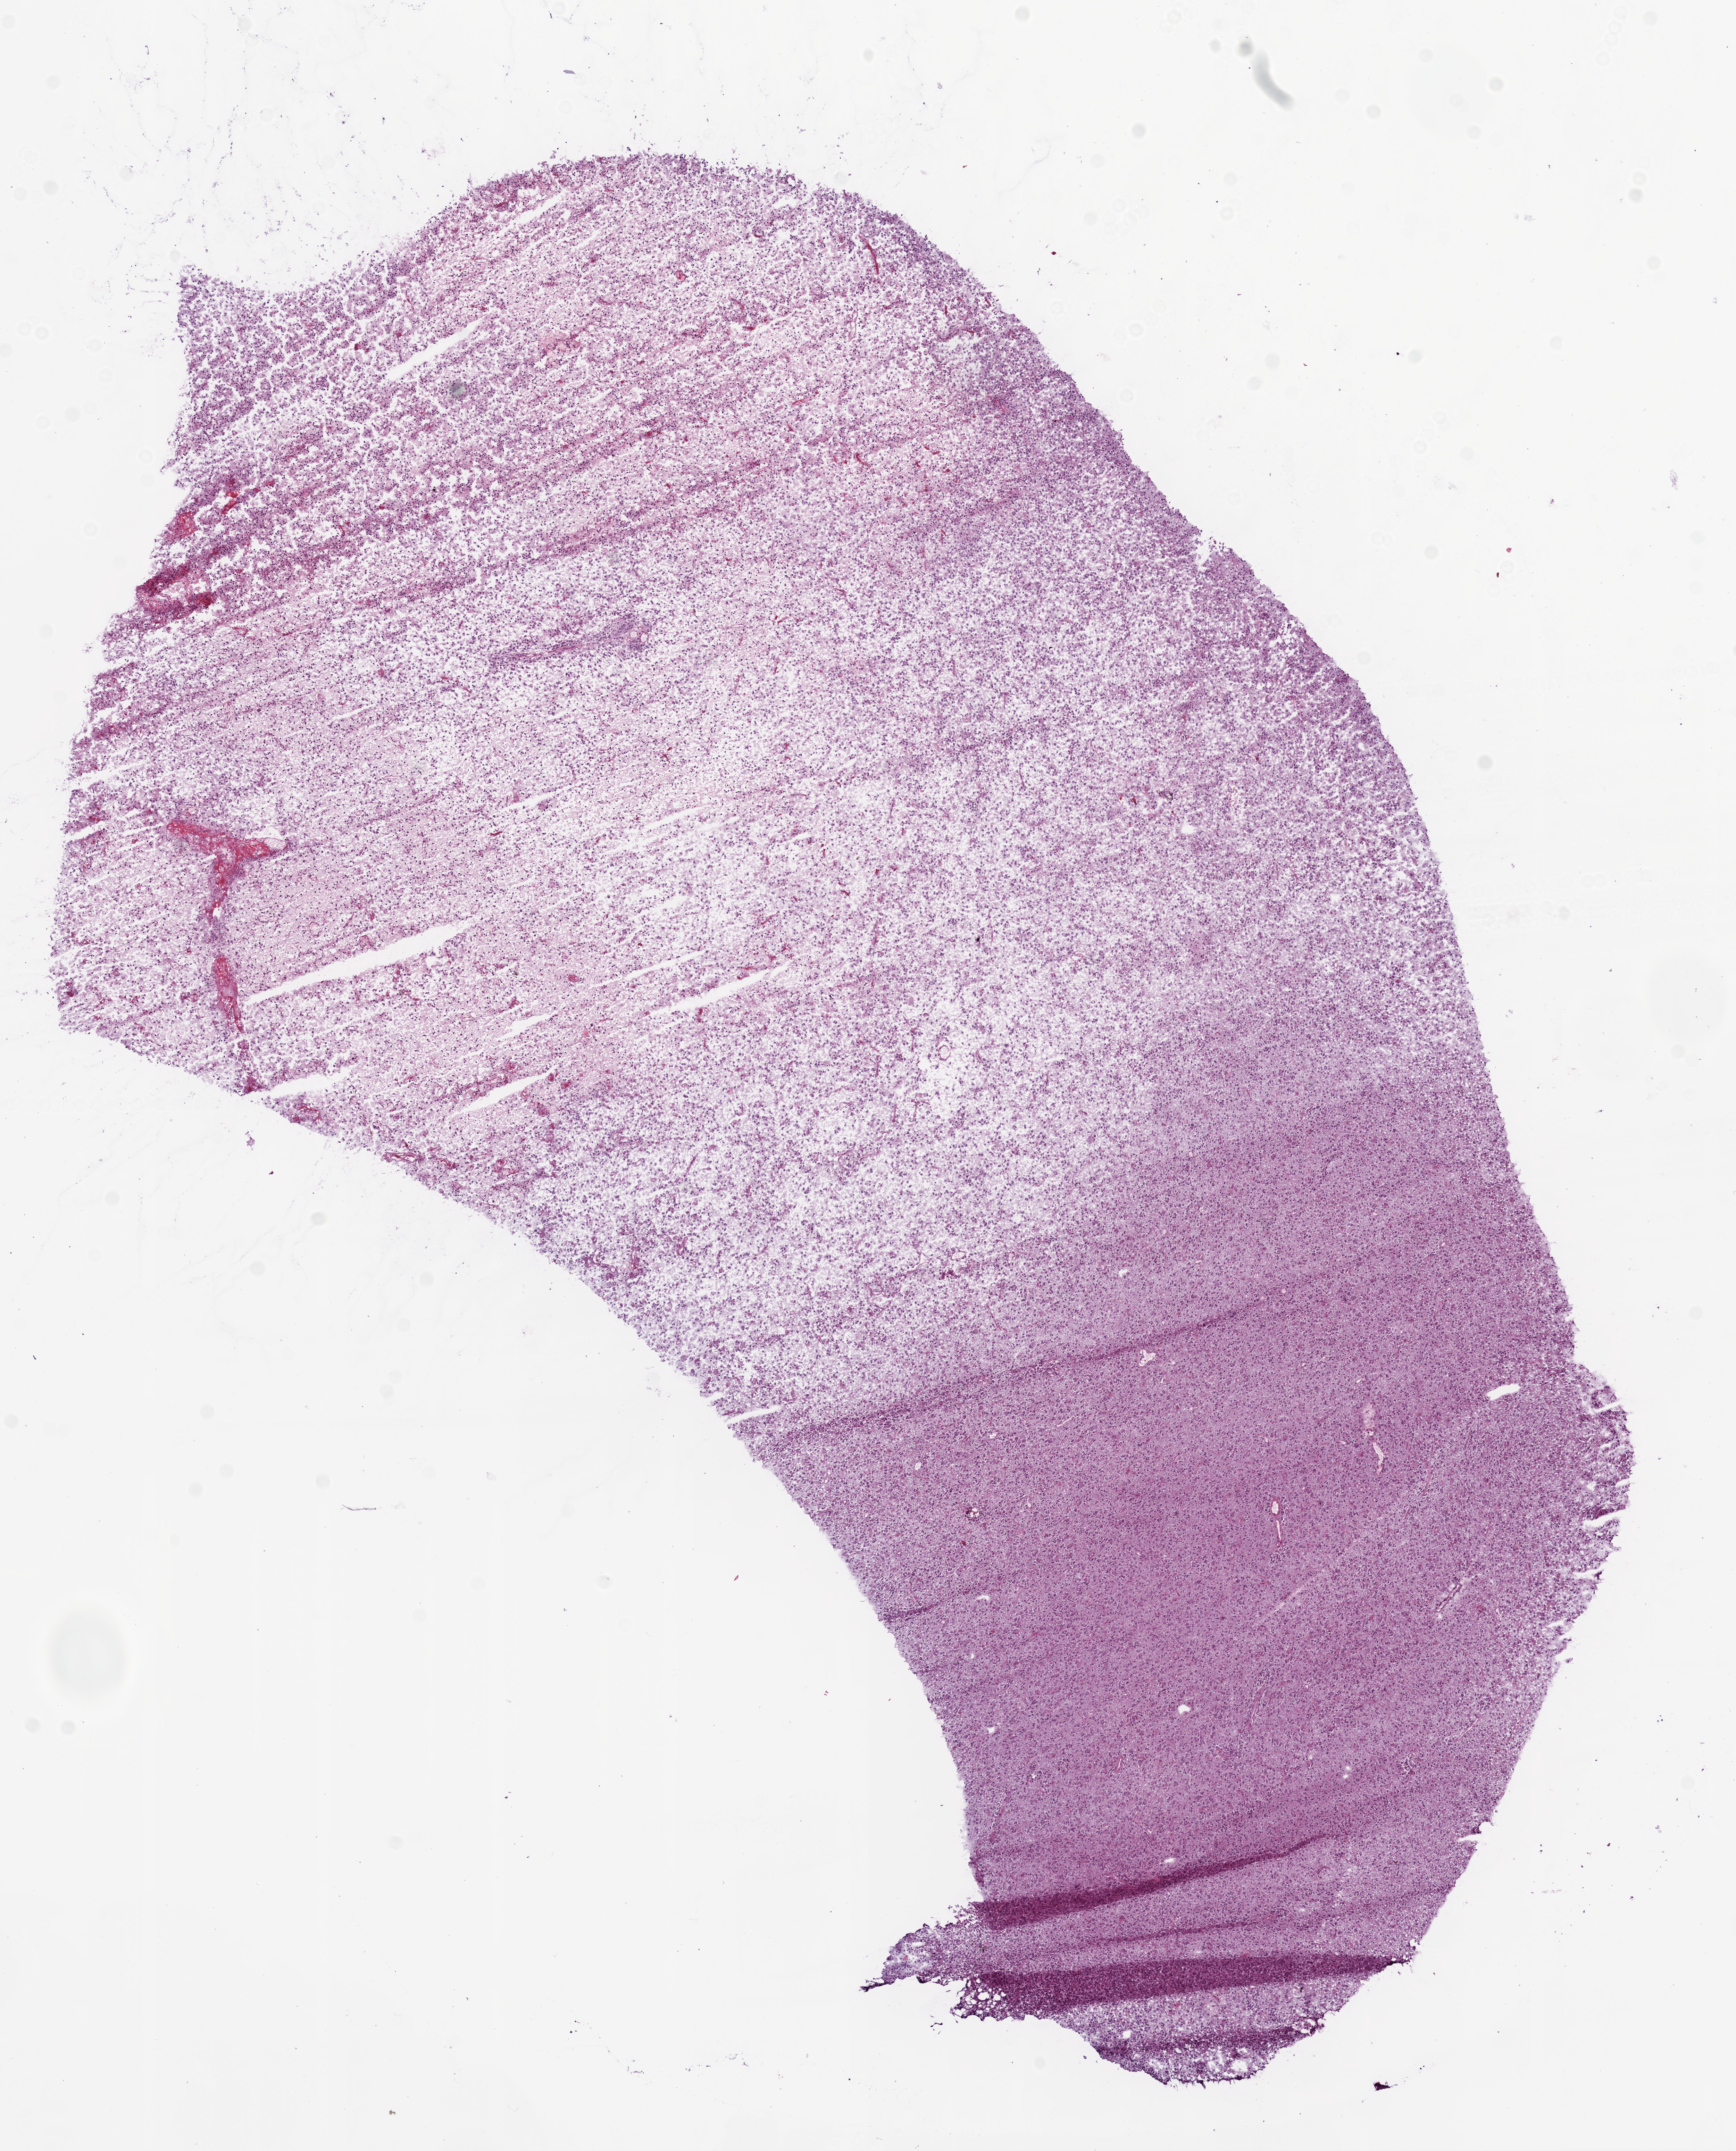
Digitized Hematoxylin and eosin (H&E) stained tissue section (whole slide), shown as a low-resolution overview of the whole scanned area (about 10.0 x 12.4 mm). Frozen section from the bottom of the tissue portion. Brain, primary tumour sample. Patient: male, age at initial diagnosis 45 years. Slide review estimates, as recorded: tumour cells 93%, tumour nuclei 80%, normal cells 0%, stromal cells 0%, necrosis 7%.
- histologic diagnosis: Glioblastoma